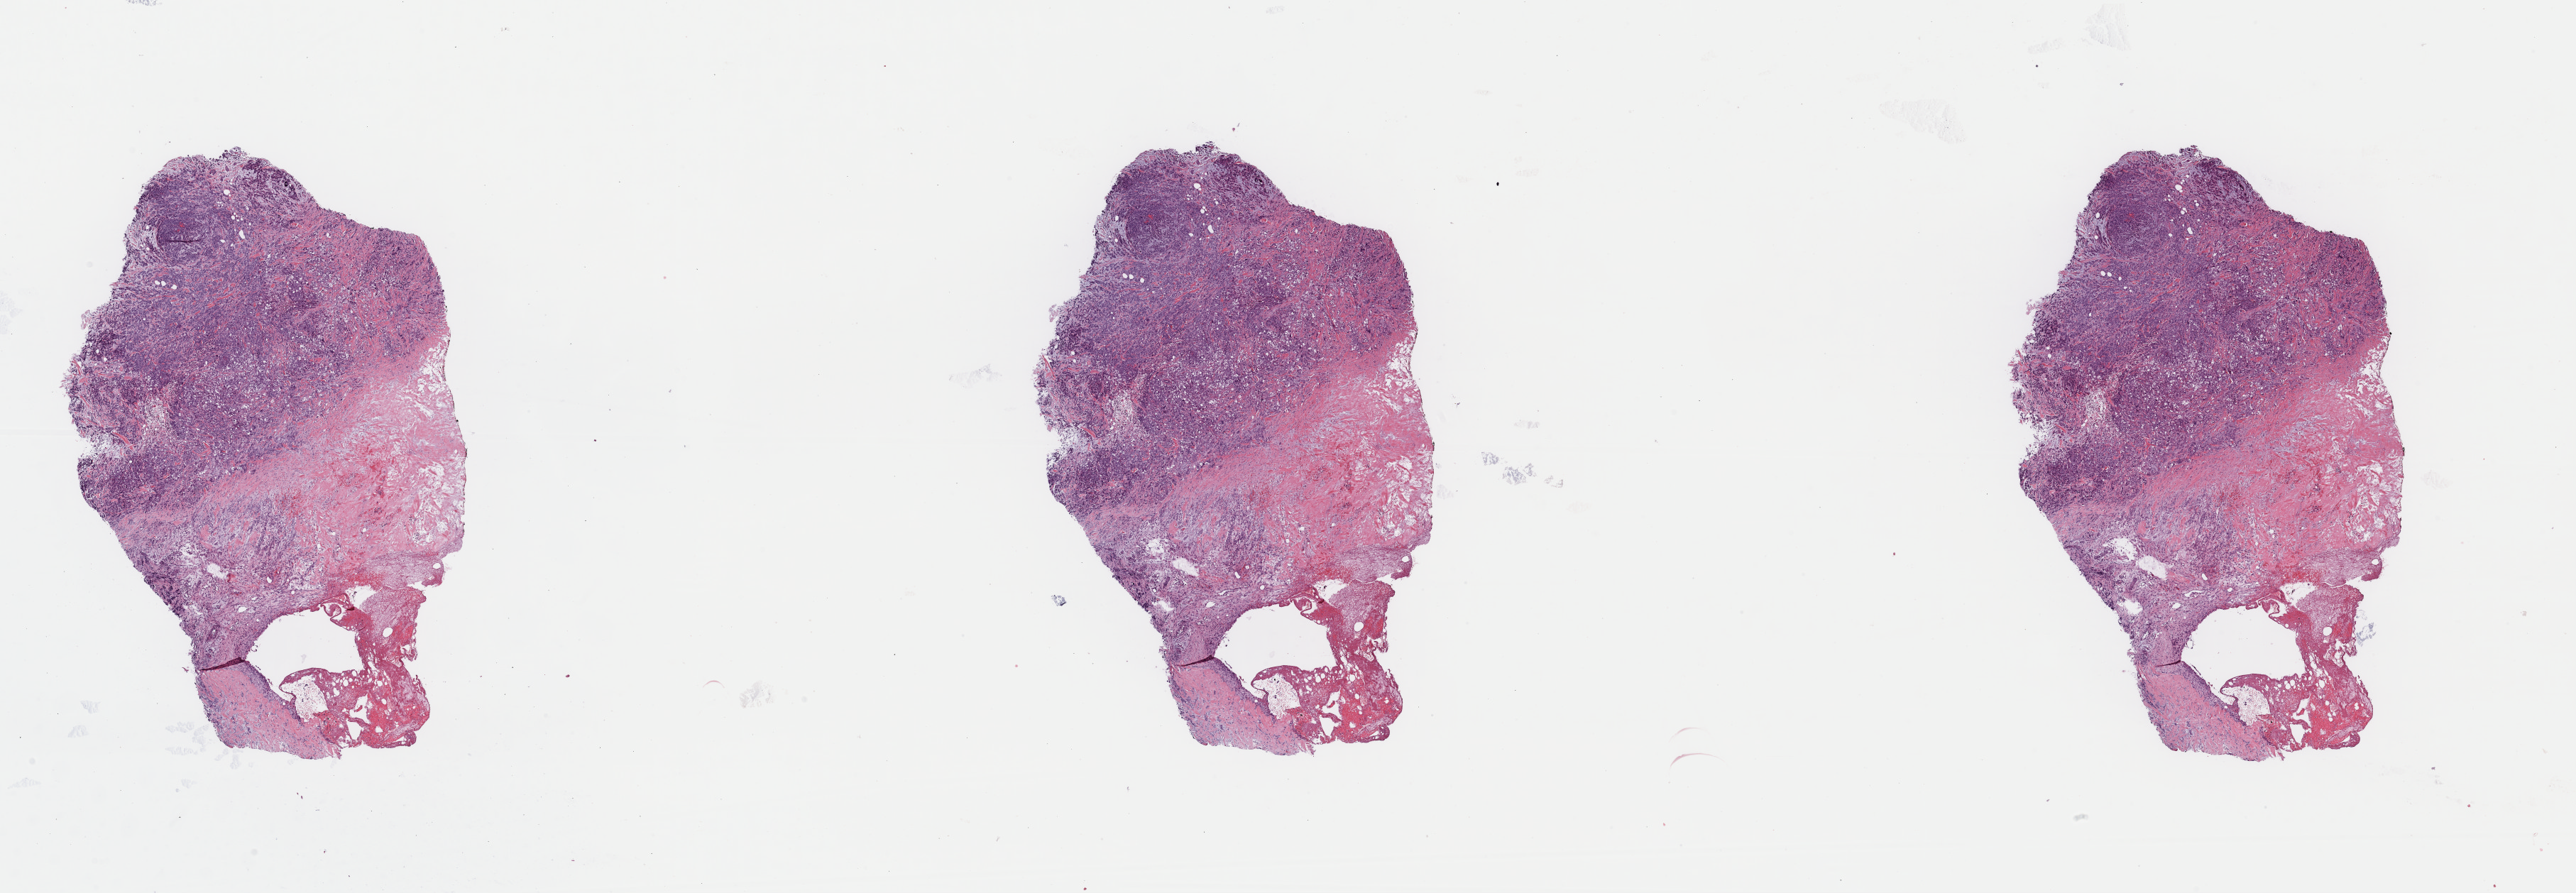
Digitized H&E tissue section (whole slide) — low-resolution overview of the scanned area, about 28.7 x 9.9 mm (slide scanned at 40x). Formalin-fixed paraffin-embedded (FFPE) diagnostic section. Sample: primary tumour, breast. Female, age 54 years at initial diagnosis.
Pathologic diagnosis: Infiltrating duct carcinoma, NOS. Laterality: left. AJCC pathologic stage: IIA.